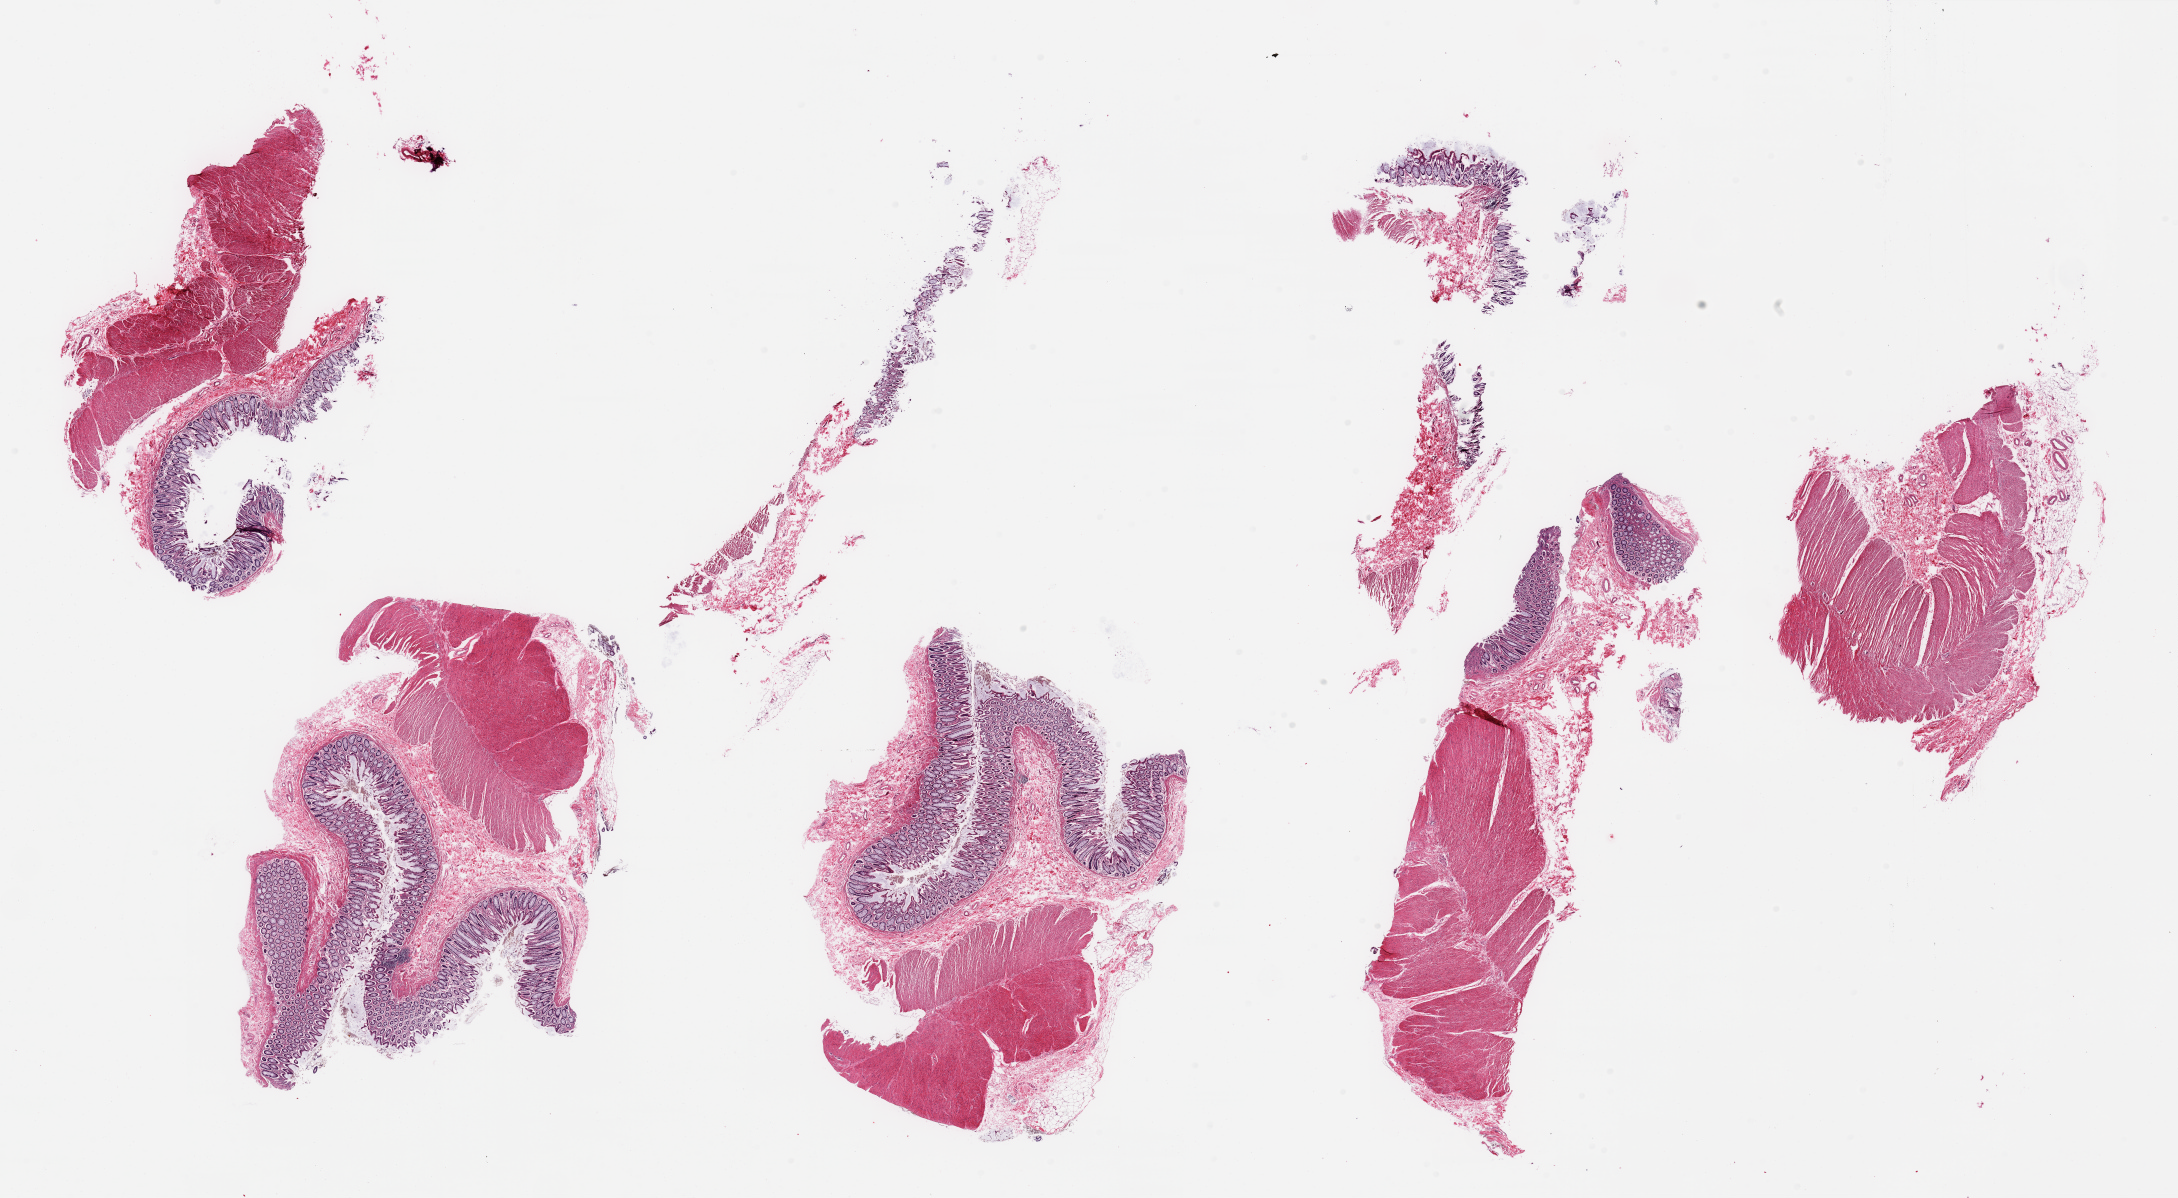
Digitized H&E-stained section — shown as a low-resolution overview of the whole scanned area (about 34.5 x 19.0 mm). PAXgene-fixed paraffin-embedded (PFPE) section. Sampled site (target tissue): sigmoid colon. Donor tissue sample.
Review note (as recorded): 5 pieces, fragmented, target muscularis present but < 50% of specimen, ~30-35%.